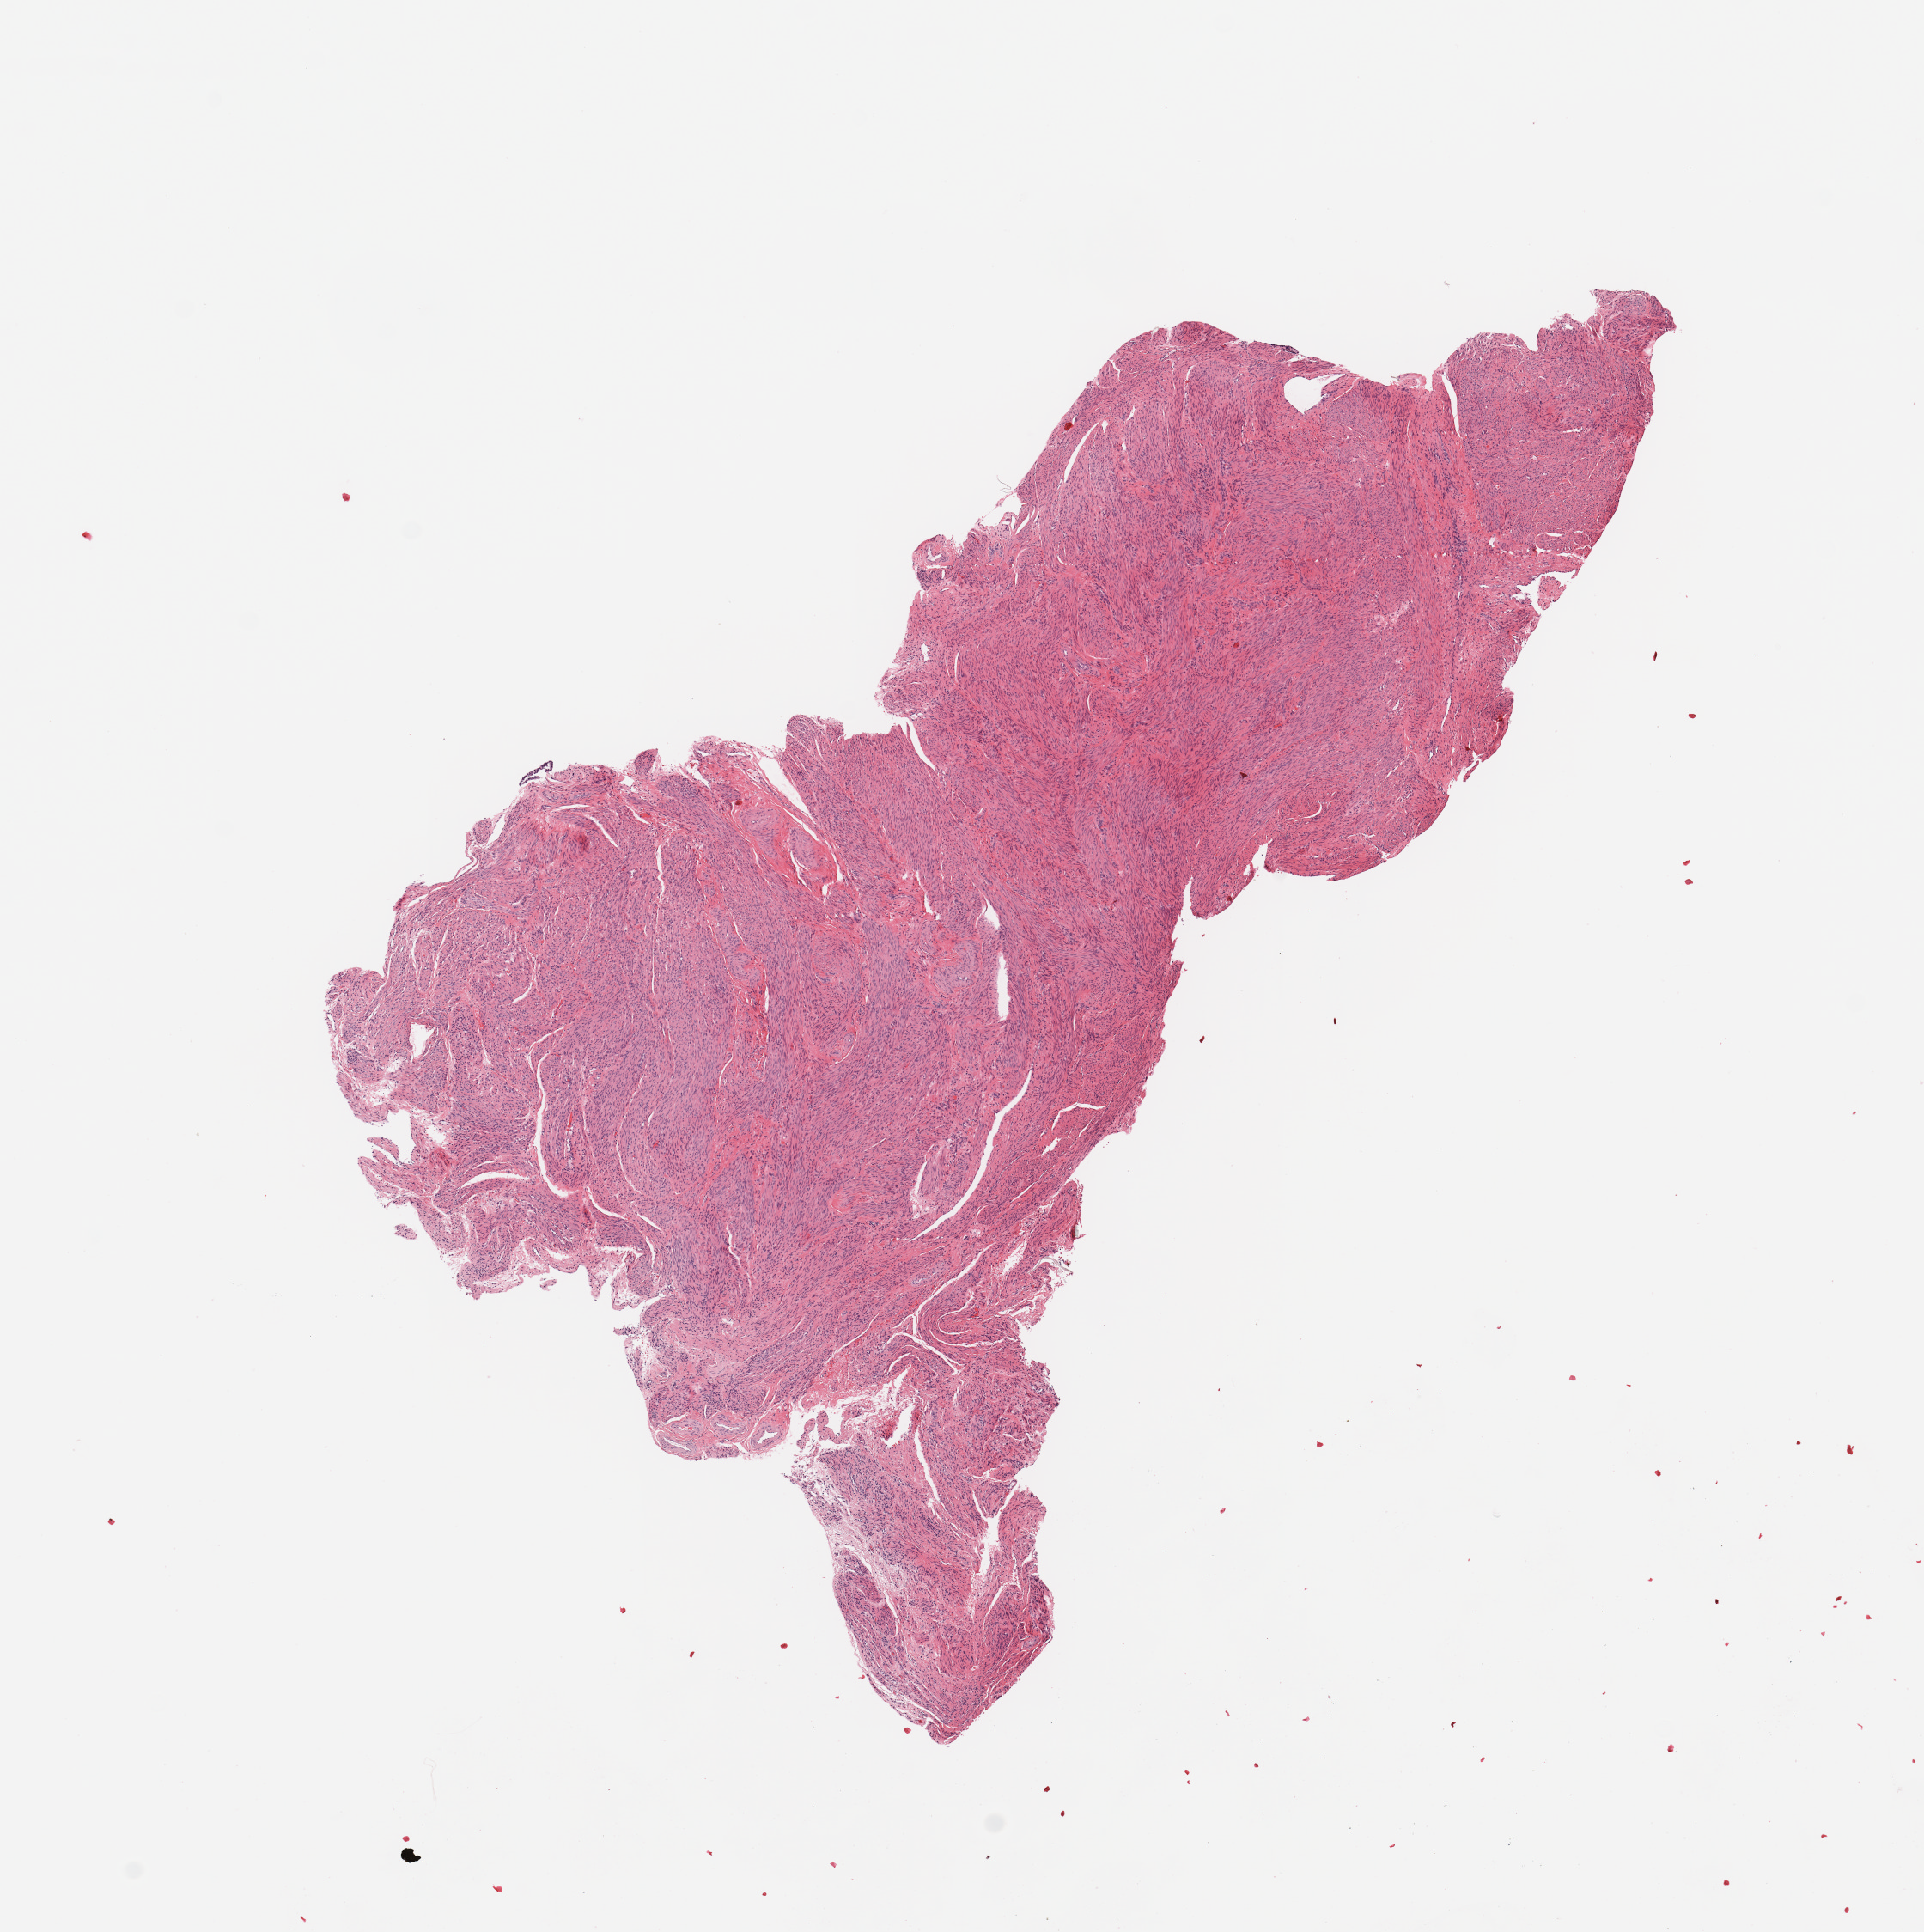
H&E-stained whole-slide image, whole scanned area (about 8.9 x 8.9 mm, from a 20x scan) shown as a low-resolution overview, normal (non-tumour) tissue sample, uterus. 64-year-old female patient.
This section: normal (non-tumour) tissue from the same patient. Patient diagnosis: Endometrioid adenocarcinoma, NOS.